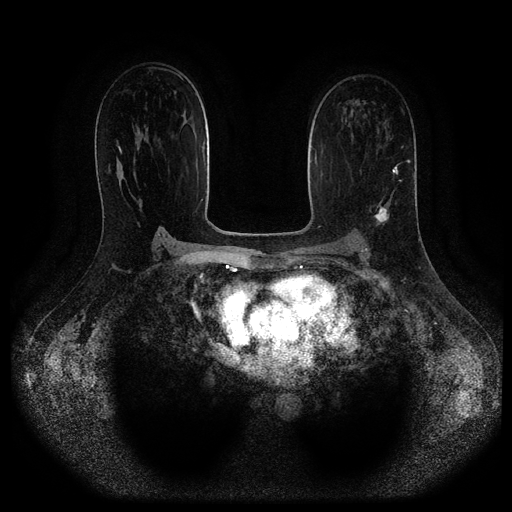
Breast MRI (dynamic contrast-enhanced, multi-phase), one axial slice. Slice 63 of 116 in the series (ordered by position). Dynamic contrast-enhanced series, time point 2 of 5 at this slice position (early post-contrast). 1.5 T. TE 2.6 ms, TR 5.3 ms. 512 × 512 image matrix, field of view 370 × 370 mm. Patient: female, 45 years.
Annotated regions visible in this slice (semi-automatic segmentation, software-assisted and operator-edited):
- breast lesion (labelled 'tumour' in the annotation; benign lesions carry a separate 'benign' label): bounding box (x1, y1, x2, y2) in pixels: (373, 205, 390, 227)